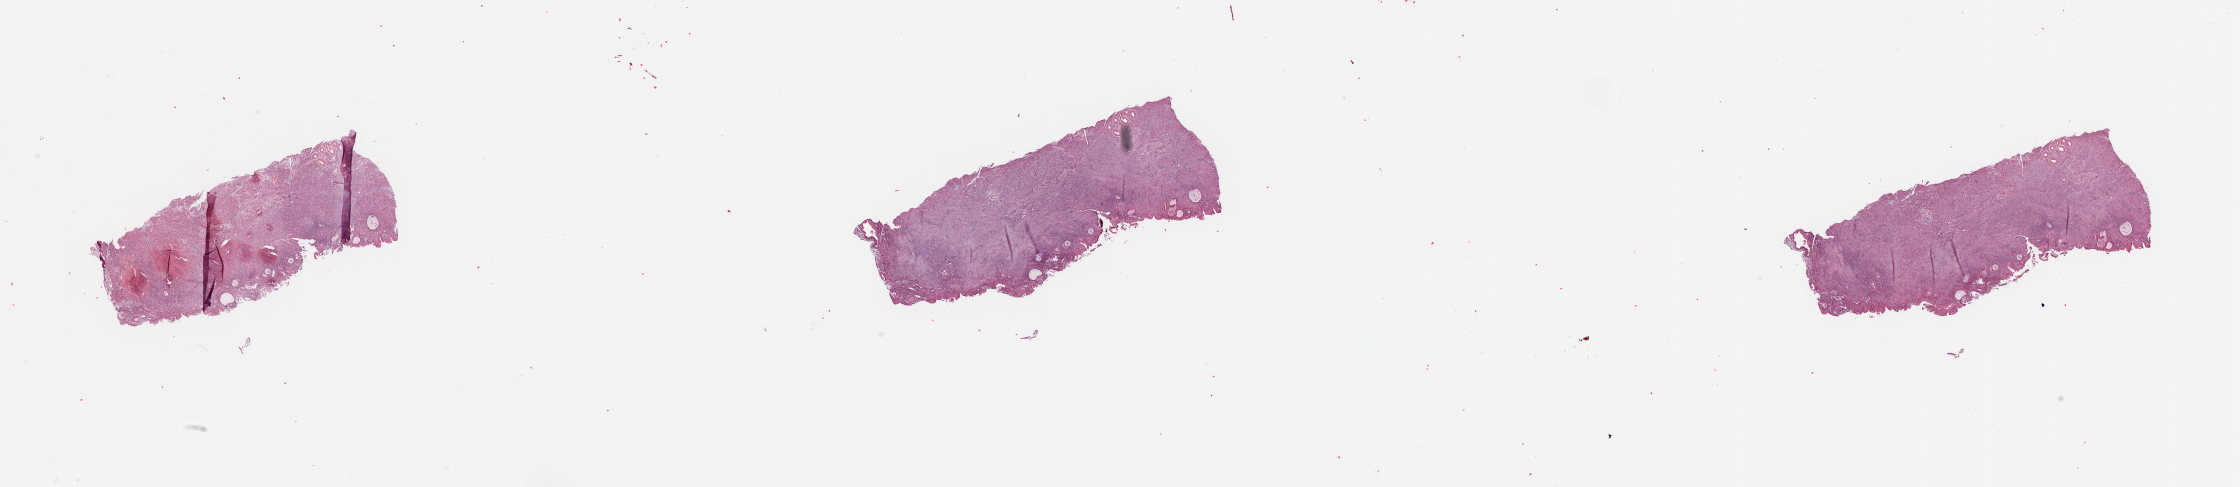
Digitized H&E tissue section (whole slide), low-resolution overview of the scanned area, about 35.4 x 7.7 mm; normal (non-tumour) tissue sample, uterus. Female, 70 y/o.
• this section: normal (non-tumour) tissue from the same patient
• patient diagnosis: Endometrioid adenocarcinoma, NOS